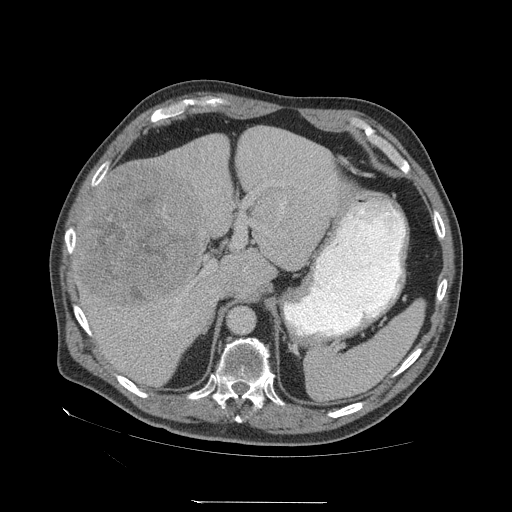
Contrast-enhanced abdominal CT (liver protocol), one axial slice; slice 42 of 83 in the series (ordered by position); 140 kVp; soft-tissue window (W 400 / L 40 HU); 2.5 mm slice thickness; 512 × 512 image matrix. From the clinical record (not read from this slice): diagnosis: hepatocellular carcinoma (patient treated with transarterial chemoembolisation; whether this scan precedes or follows treatment is not stated here); TNM stage (as recorded): Stage-I; Child-Pugh class: A; tumour differentiation: well differentiated.
Annotated regions visible in this slice (semi-automatically segmented with operator editing):
- liver parenchyma outside the tumour (the mass and vessels are separate outlines, so this box may not span the whole liver): bounding box [x1, y1, x2, y2] px = [72, 126, 340, 386]
- mass: [77, 162, 205, 309]
- liver vessels: [84, 202, 285, 335]